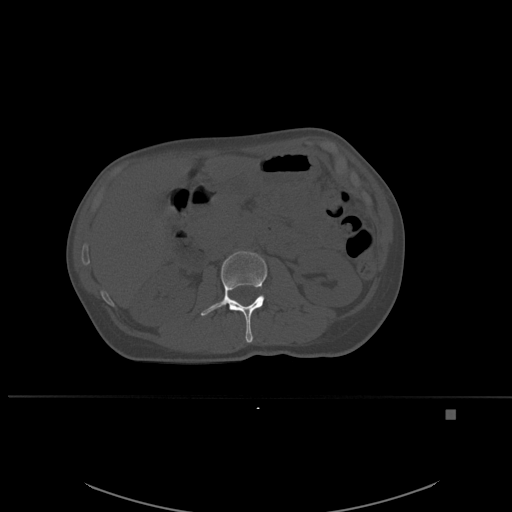
CT including the spine, one axial slice. Slice 235 of 537 in the series (ordered by position). Bone window (W 1800 / L 400 HU). 512 × 512 image matrix, field of view 440 × 440 mm. Patient: female, 45 years. From the clinical record (not read from this slice): primary cancer: lung.
Structures marked on this image (semi-automatic segmentation, software-assisted and operator-edited):
- L2 vertebra: bounding box [x1, y1, x2, y2] px = [201, 251, 268, 343]